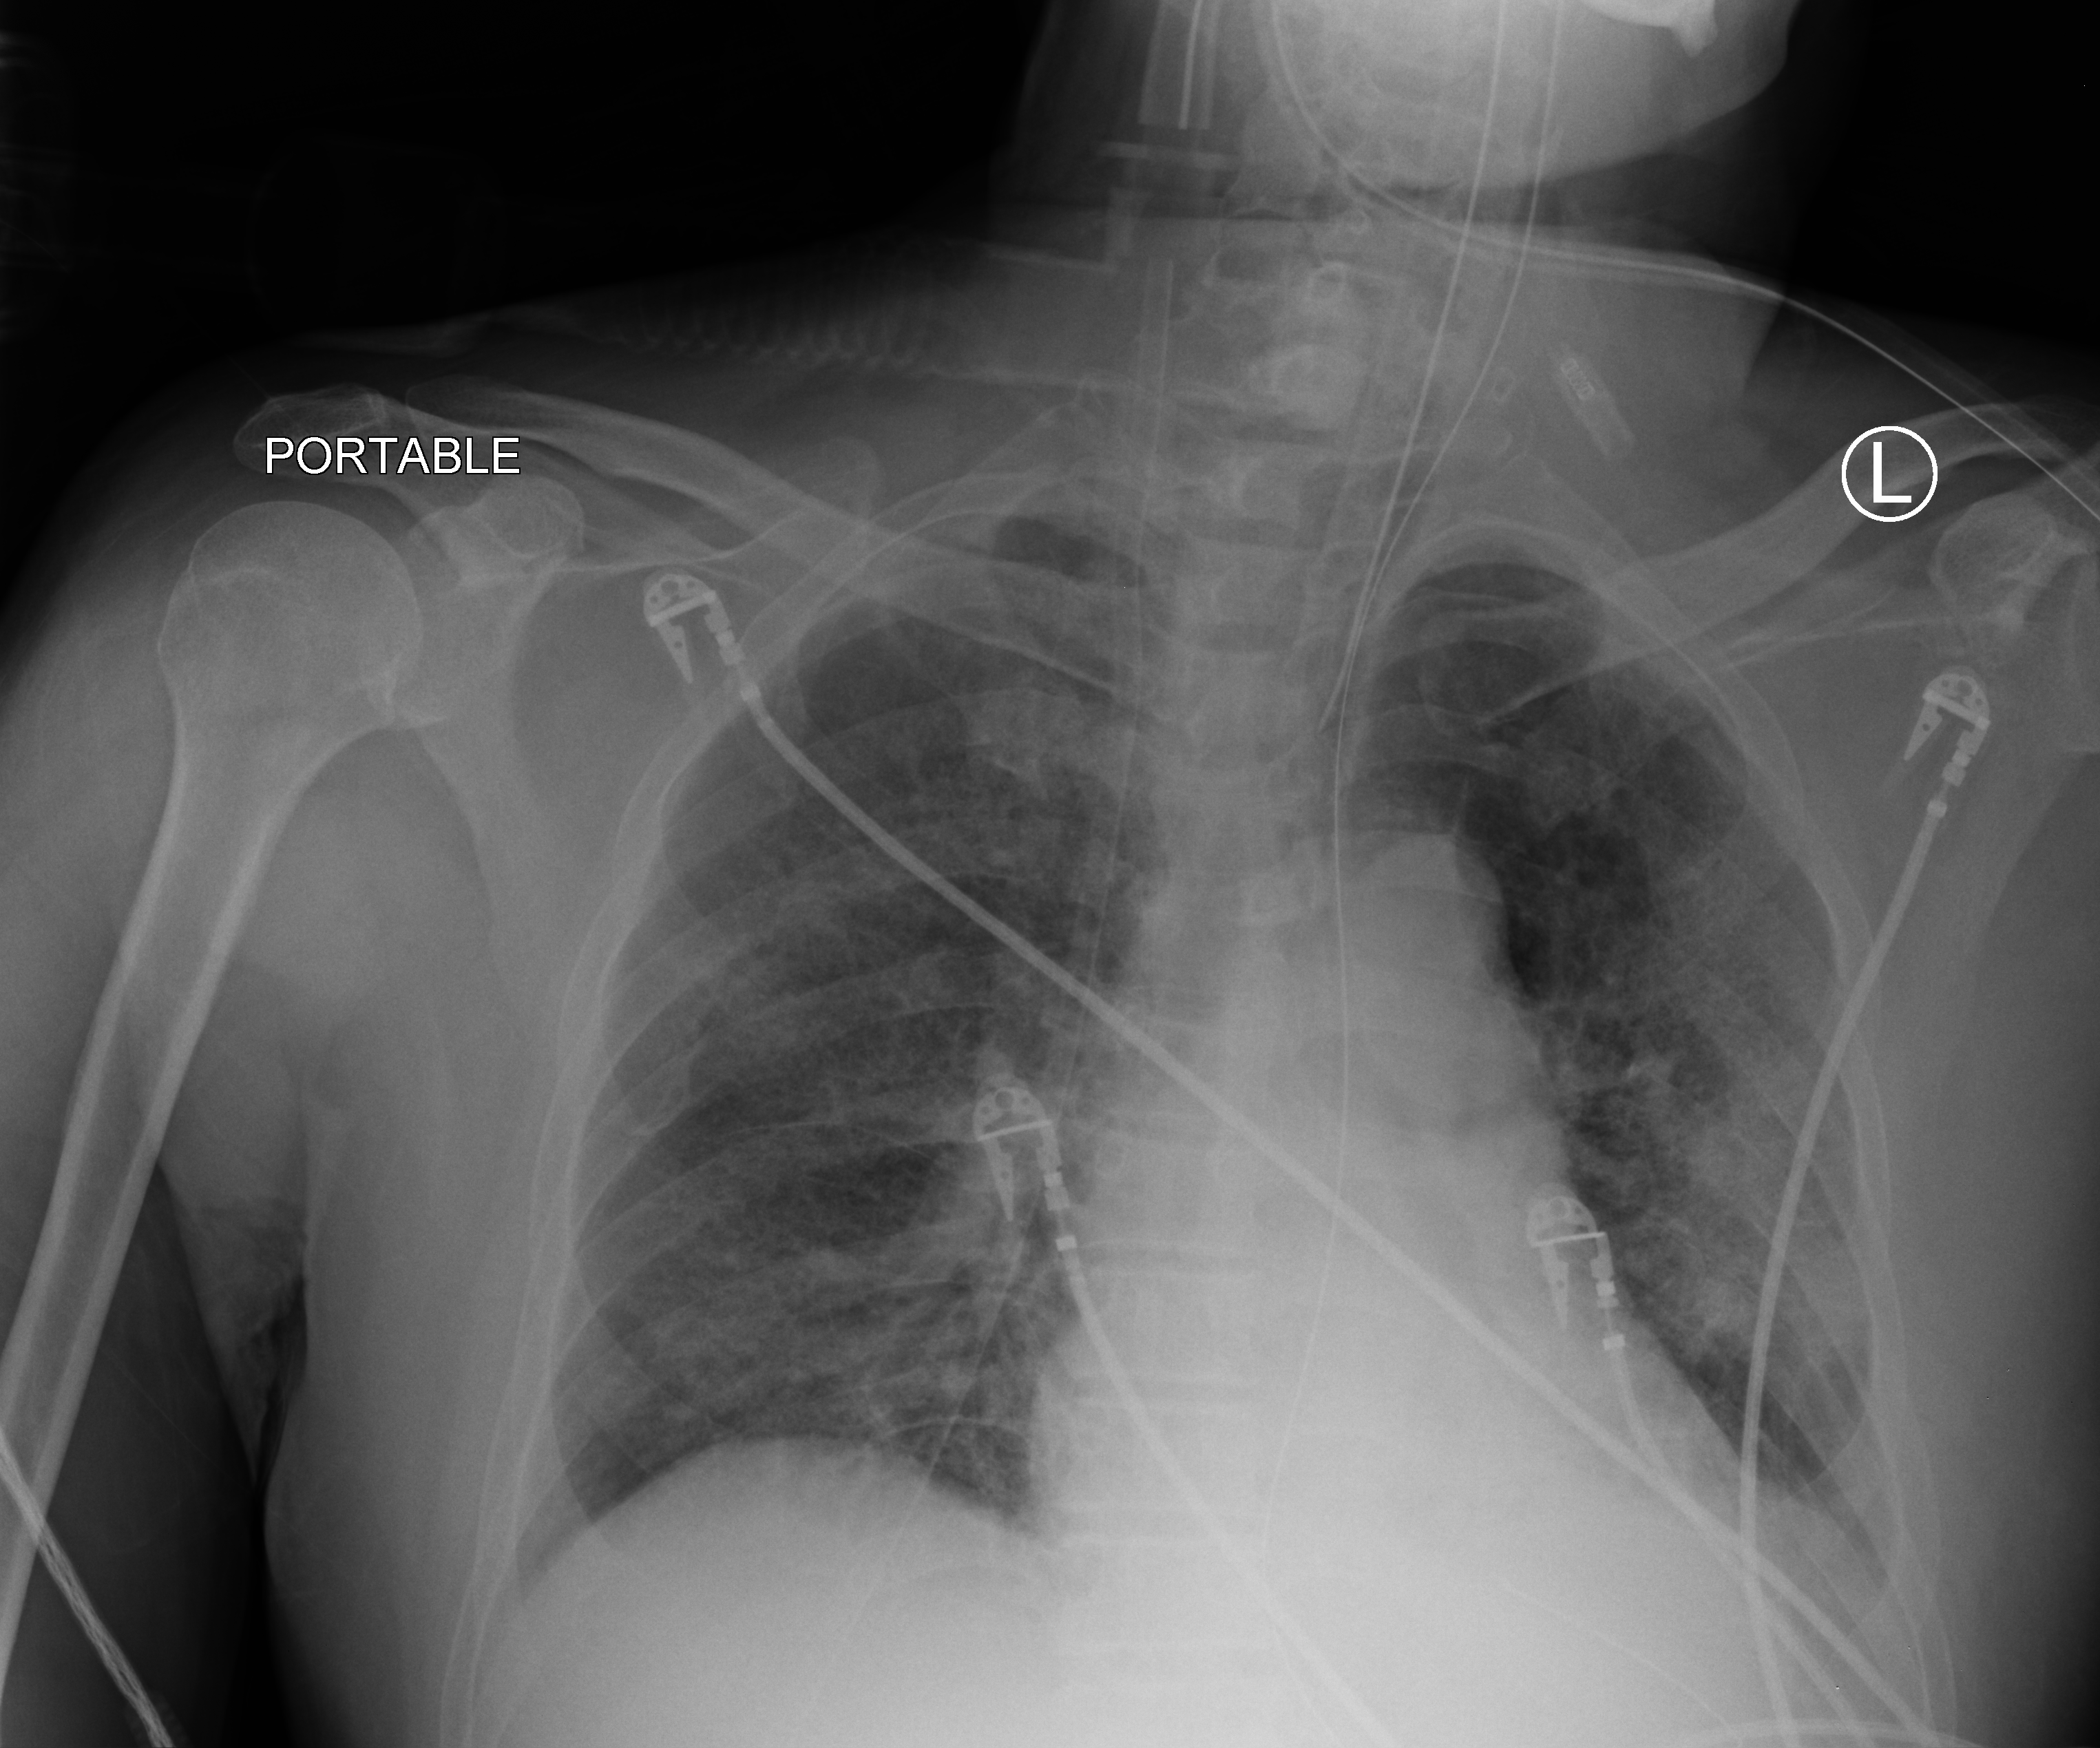
Bedside chest radiograph (computed radiography). Patient hospitalised with COVID-19; male, aged 60–74 years.
Hospital-stay facts (about this admission, not read from this image; timing relative to this image not recorded):
- length of hospital stay: 14 days
- admitted to intensive care during this hospital stay: yes